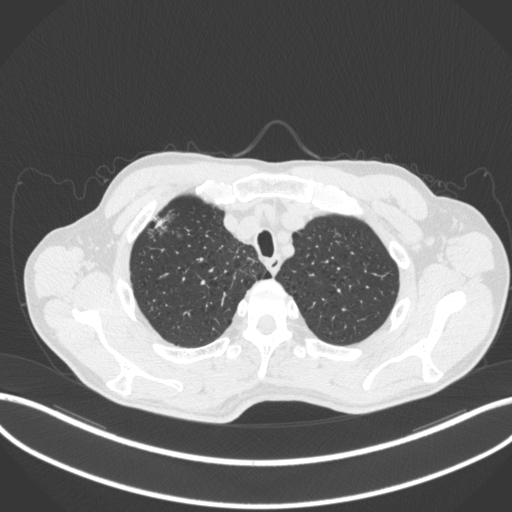
Chest CT, one axial slice; slice 363 of 414 in the series (ordered by position); reconstruction kernel B31f; 120 kVp; lung window (W 1500 / L -600 HU); 512 × 512 image matrix, field of view 400 × 400 mm. Patient: male, 69 years. From the clinical record (not read from this slice): clinical TNM (as recorded): T1b N1 M0.
Structures marked on this image (bounding box drawn by a radiologist):
- lung tumour (recorded histology: adenocarcinoma): bounding box (x1, y1, x2, y2) in pixels: (147, 216, 169, 234)